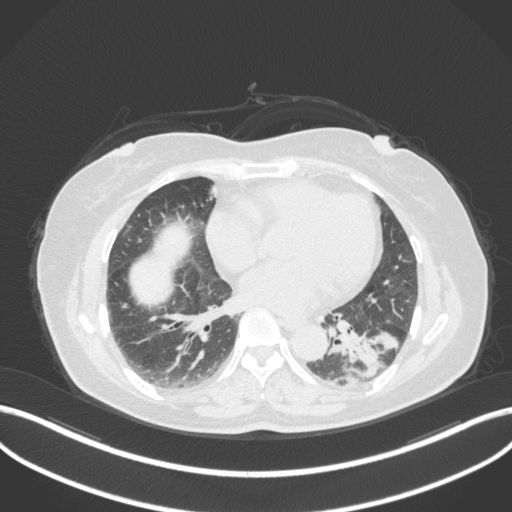
Chest CT, one axial slice; slice 155 of 307 in the series (ordered by position); lung window (W 1500 / L -600 HU); 1 mm slice thickness; 512 × 512 image matrix, field of view 400 × 400 mm. Female patient, age 59 years. Case-level facts recorded for this patient, not image findings: clinical TNM (as recorded): T2a N0 M0; histopathological grade: G2-3.
Annotated regions visible in this slice (rectangle marked by the reading radiologist):
- lung tumour (recorded histology: adenocarcinoma): bounding box (x1, y1, x2, y2) in pixels: (328, 324, 401, 395)